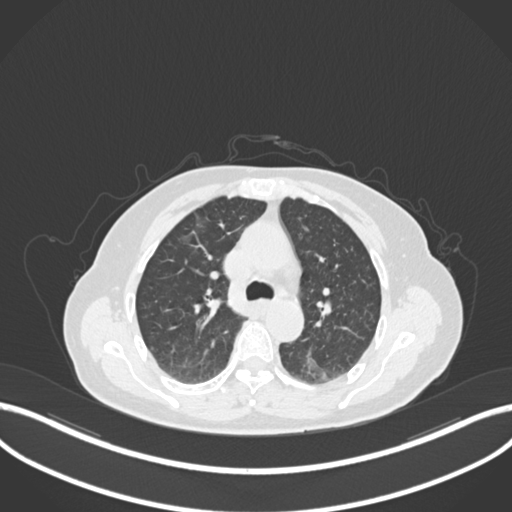
Chest CT, one axial slice; position 547 of 727 along the scan axis; reconstruction kernel B30f; lung window (W 1500 / L -600 HU); 1 mm slice thickness; 512 × 512 image matrix. Patient: female, 70 years. Case-level facts recorded for this patient, not image findings: clinical TNM (as recorded): T1c N0 M0.
Structures marked on this image (rectangle marked by the reading radiologist):
- lung tumour (recorded histology: adenocarcinoma): box from (x=303, y=355) to (x=331, y=385) px